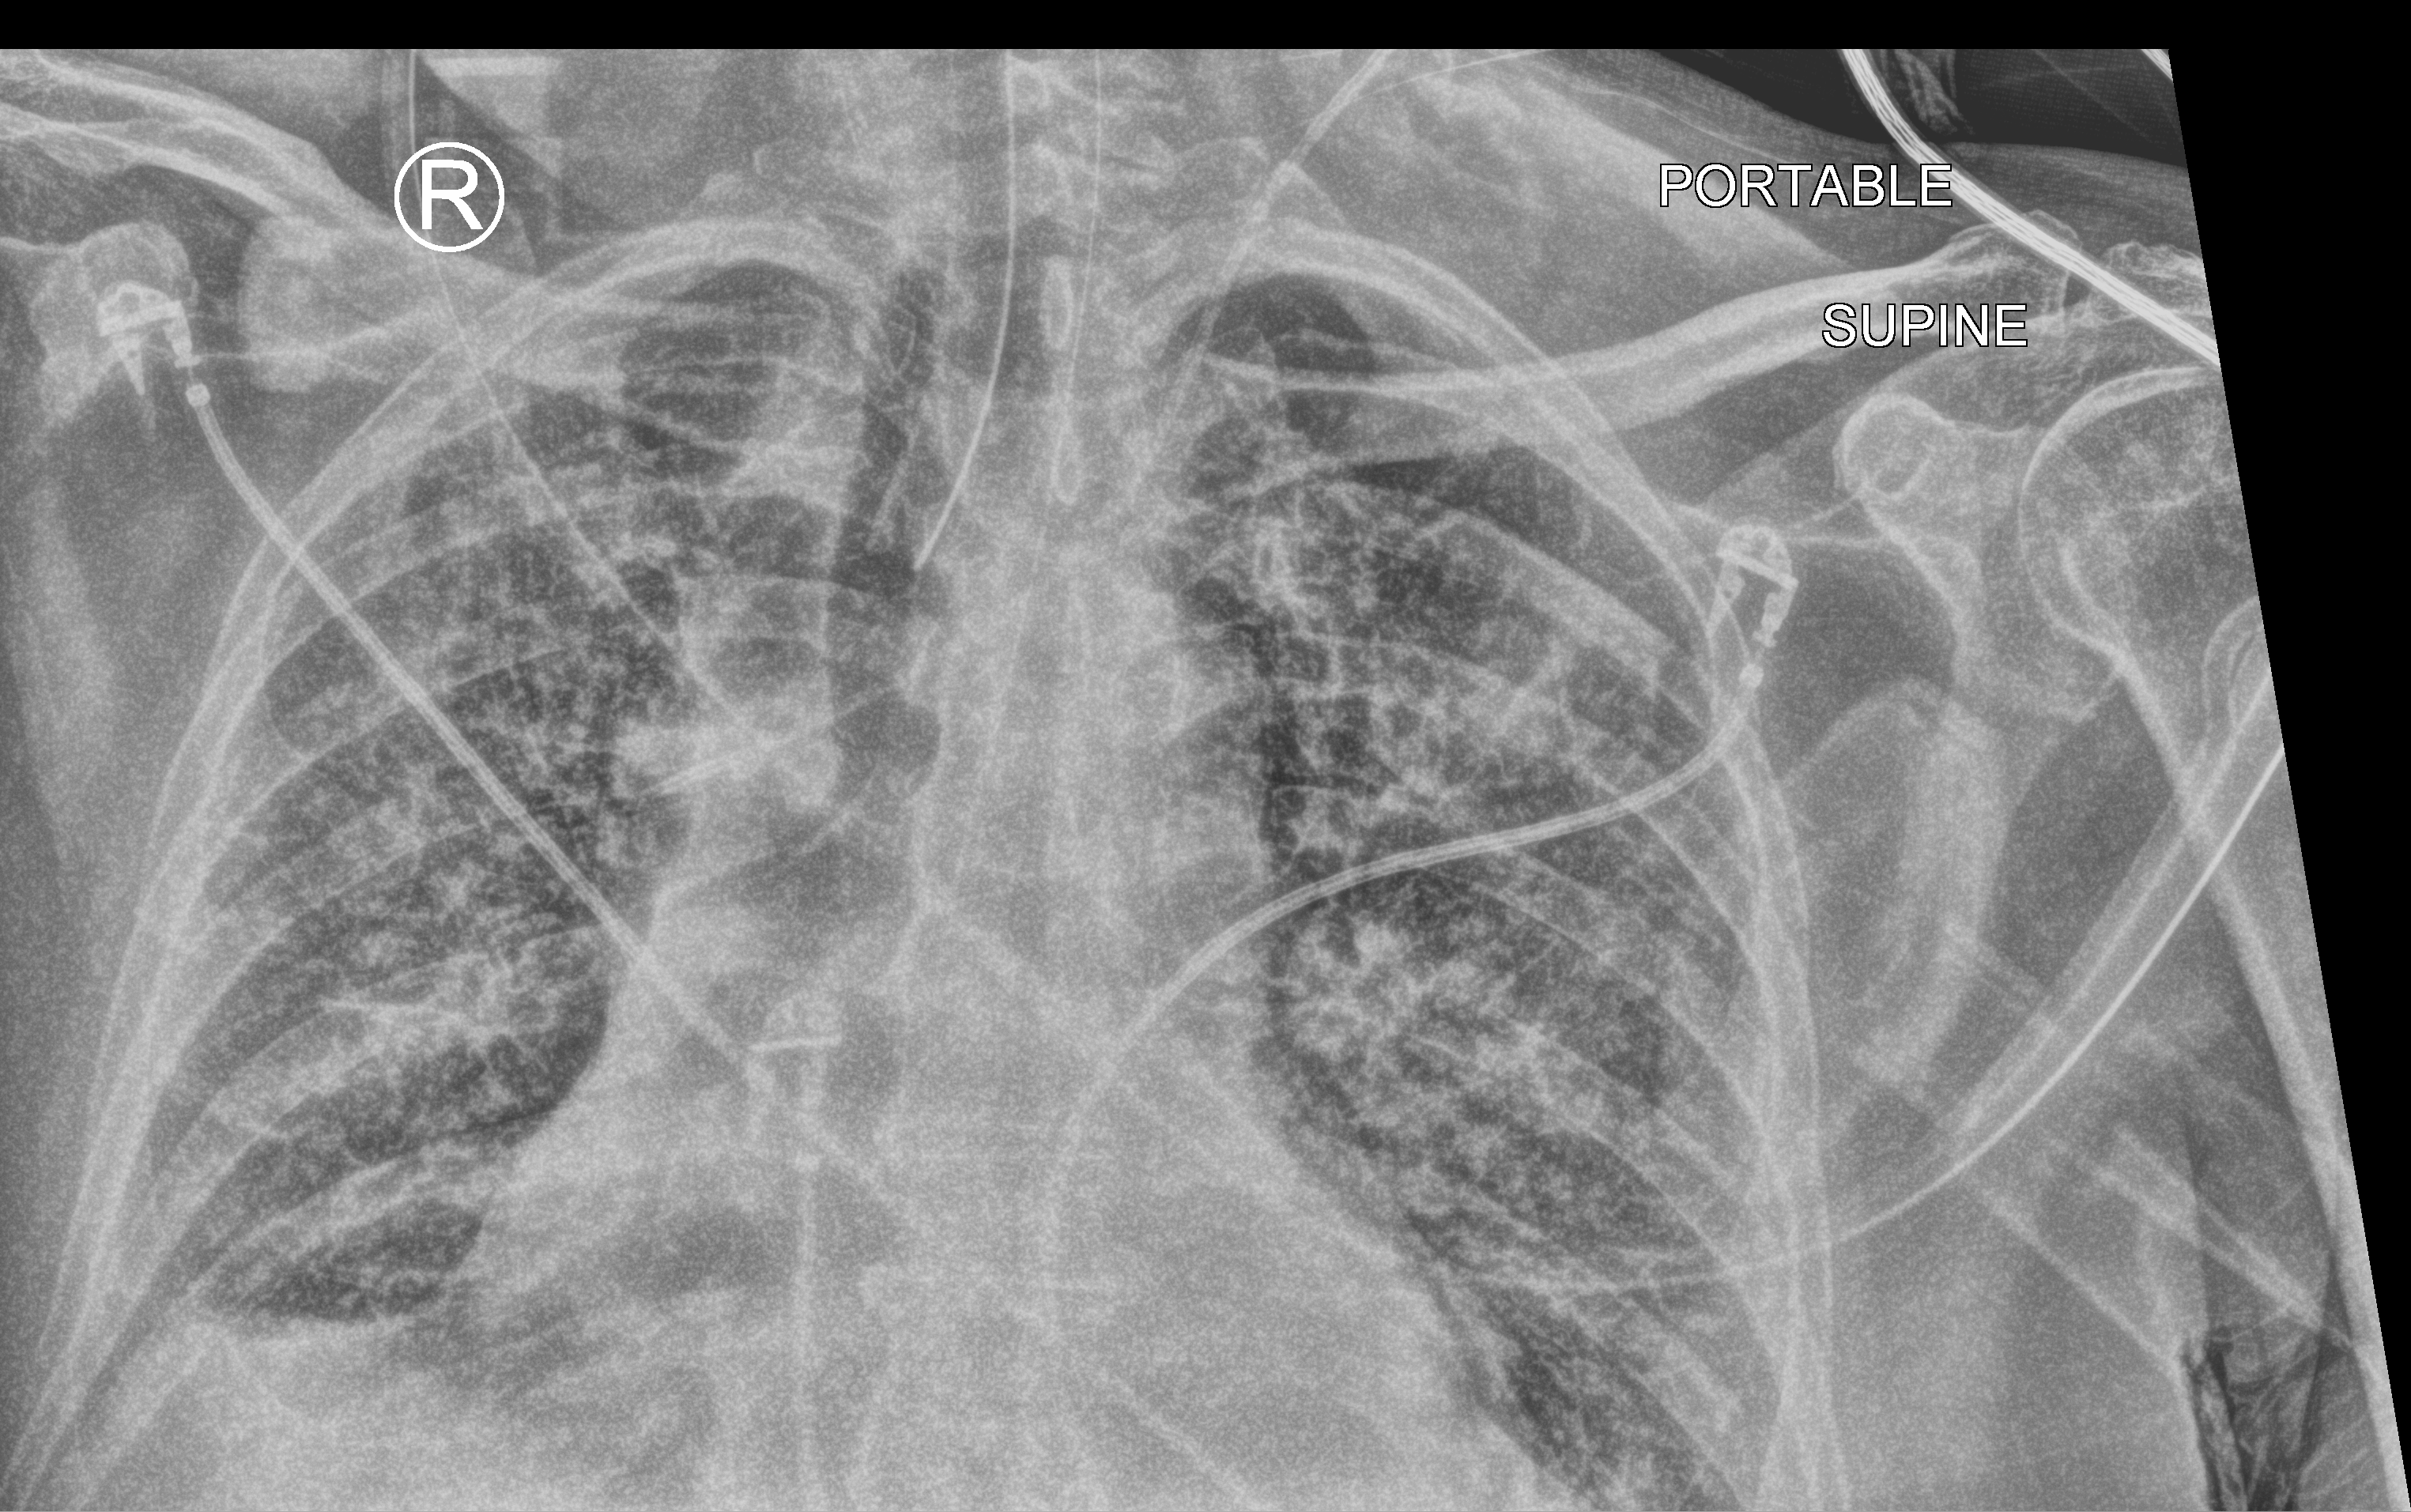
Bedside chest radiograph (computed radiography); anteroposterior (AP) projection. Male patient hospitalised with COVID-19, age 75–90 years.
Admission-level facts for this patient (not findings on this image; timing relative to this image not recorded):
- COPD (admission record): no